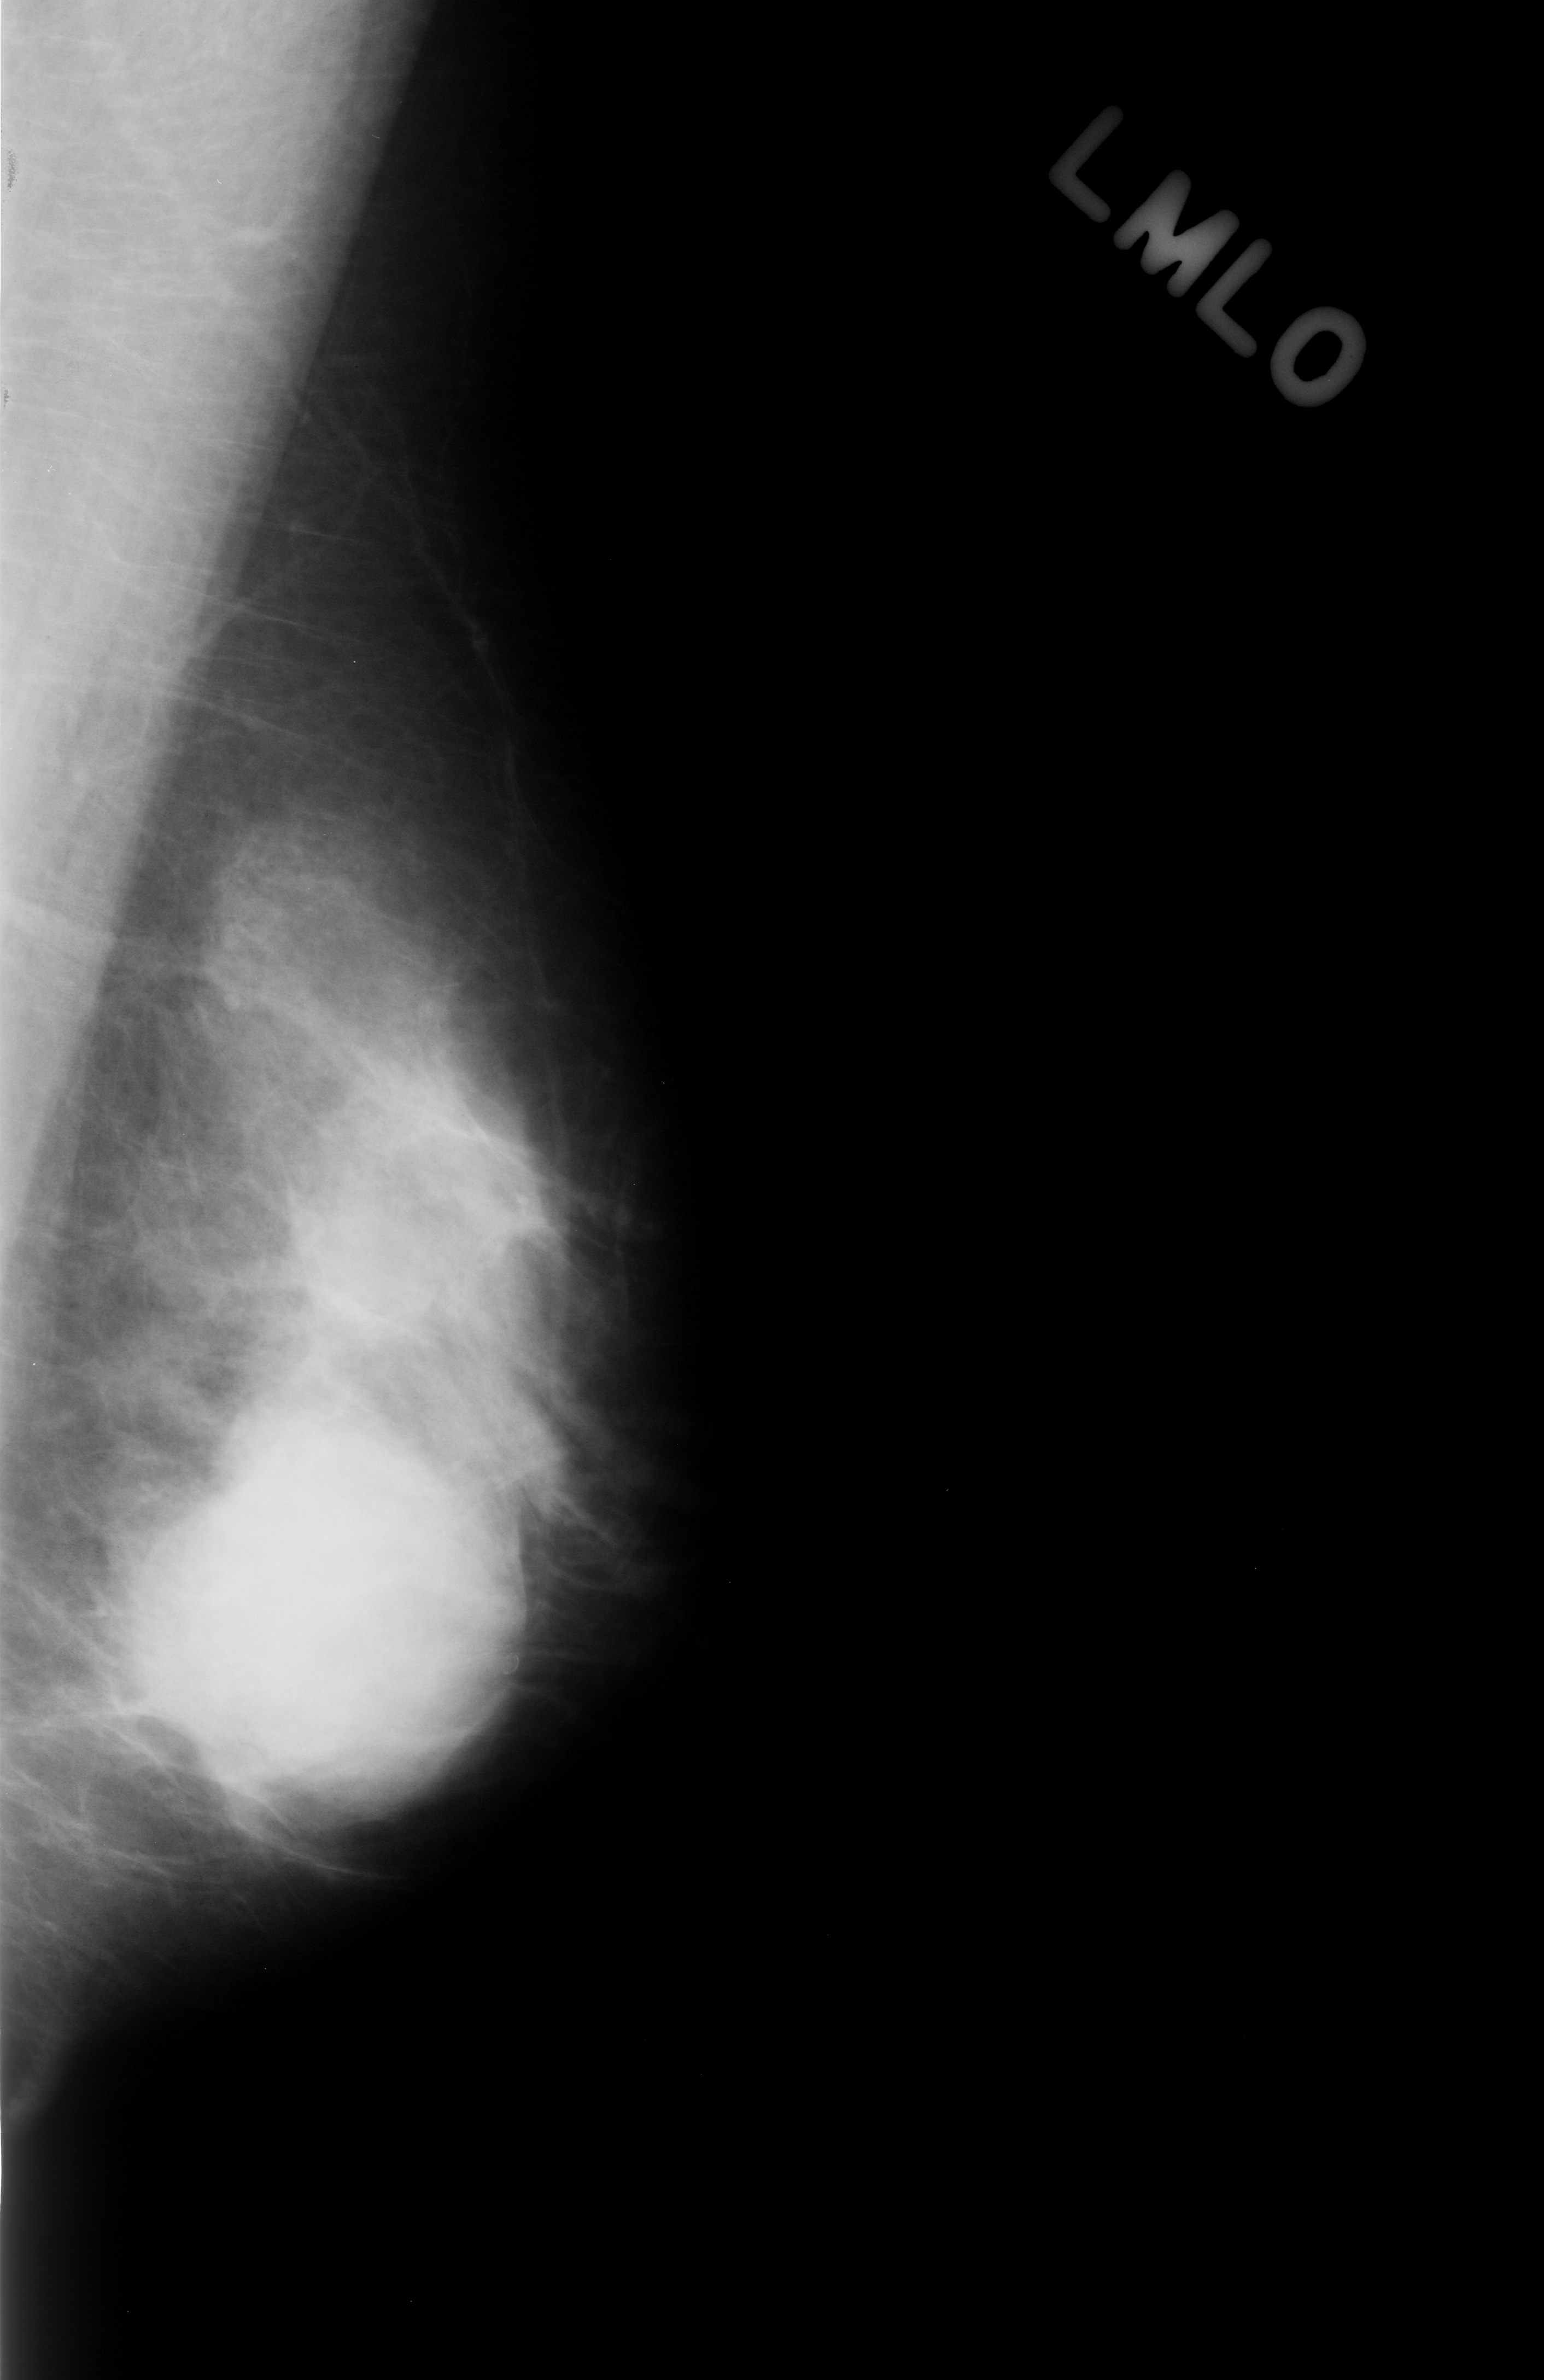
Scanned film-screen mammogram; left breast; mediolateral oblique (MLO) view; BI-RADS breast density category 4 (scale 1–4).
- Abnormality record for this image: mass, shape round, margins obscured; BI-RADS assessment category 4; subtlety rating 5 on a 1 (subtle) to 5 (obvious) scale; pathology result (as recorded, not read from the image): benign.